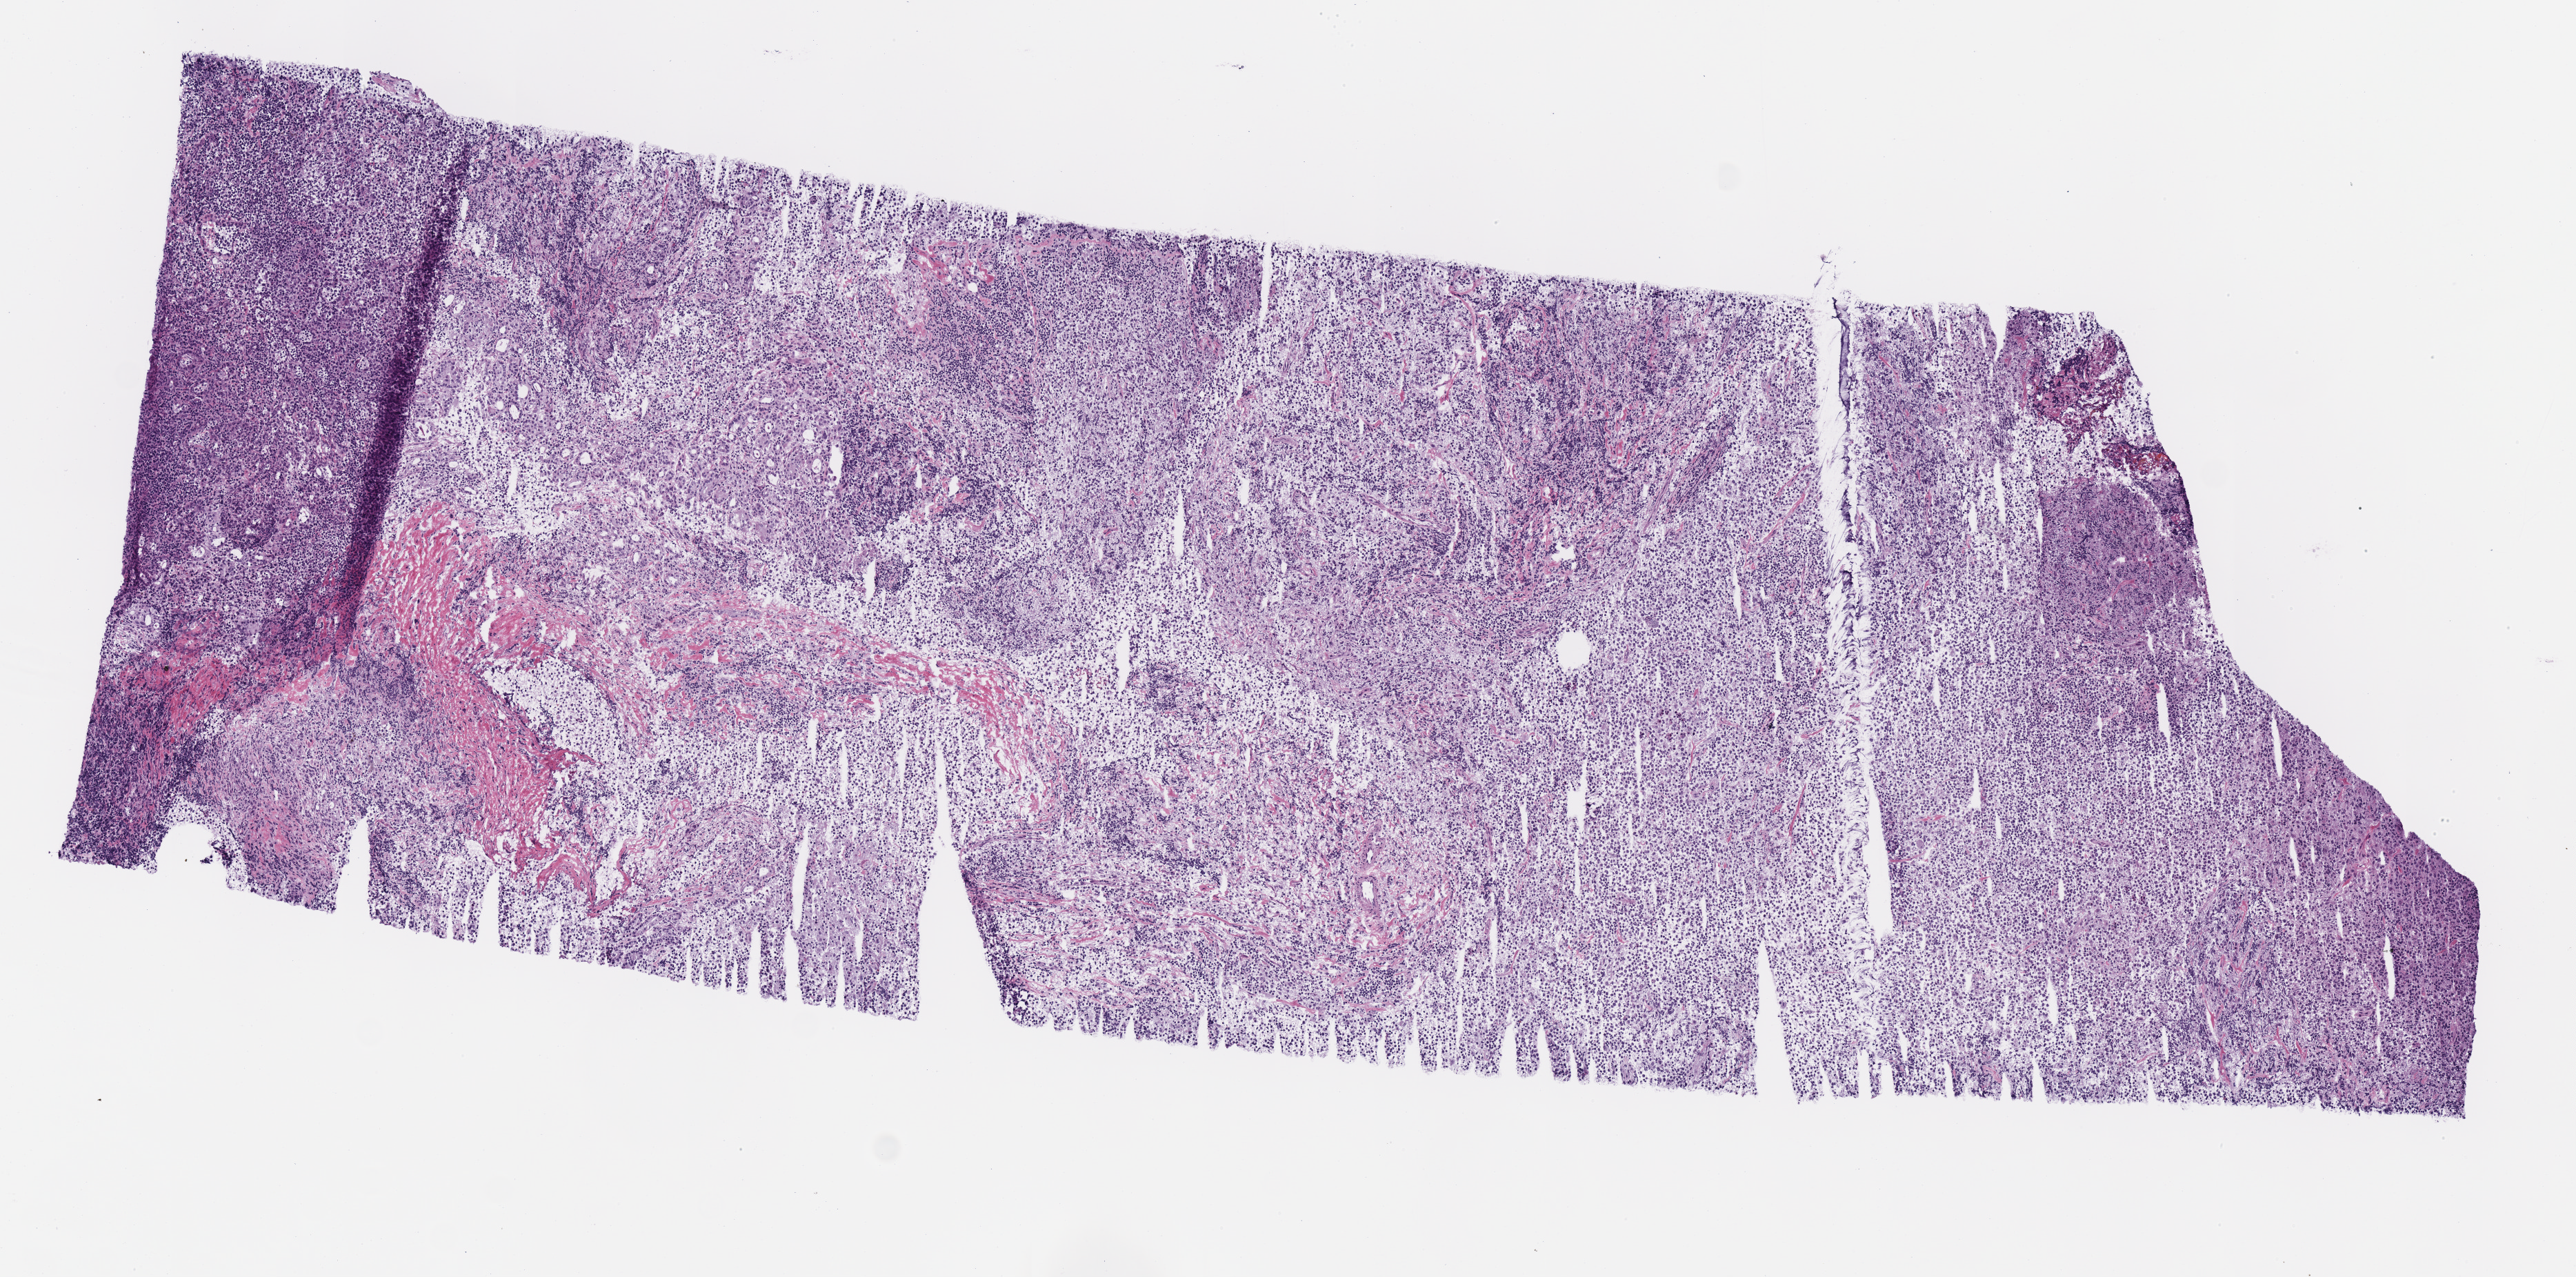
Whole-slide histology image, H&E, shown as a low-resolution overview of the whole scanned area (about 7.3 x 3.6 mm, from a 40x scan). Frozen section from the top of the tissue portion. Sample: primary tumour, lymphoid tissue. Patient: female, age at initial diagnosis 60 years. Slide review estimates, as recorded: tumour cells 90%, tumour nuclei 95%, normal cells 5%, stromal cells 5%, necrosis 0%. Inflammatory infiltration, as recorded: lymphocyte infiltration 1%.
* histologic diagnosis: Diffuse large B-cell lymphoma, NOS (thyroid gland)